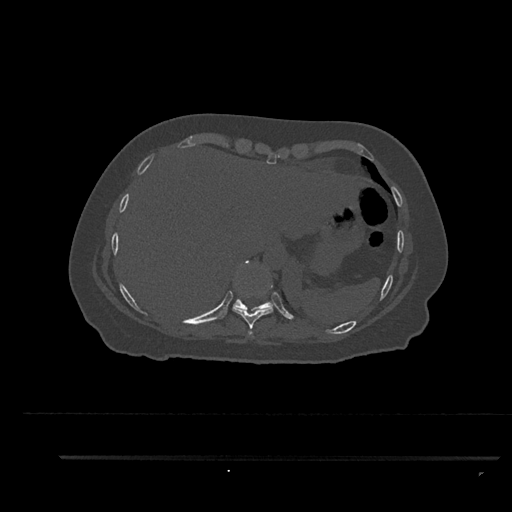
CT including the spine, one axial slice; slice 396 of 797 in the series (ordered by position); 120 kVp; bone window (W 1800 / L 400 HU); 0.5 mm slice thickness; 512 × 512 image matrix. Patient: female, 44 years. Case-level facts recorded for this patient, not image findings: primary cancer: renal; vertebrae with lytic lesions (as recorded): L1.
Structures marked on this image (semi-automatic segmentation, software-assisted and operator-edited):
- T10 vertebra: bounding box <233,260,275,311> (left, top, right, bottom; pixels)
- T8 vertebra: <248,331,253,335>
- T9 vertebra: <233,269,273,329>